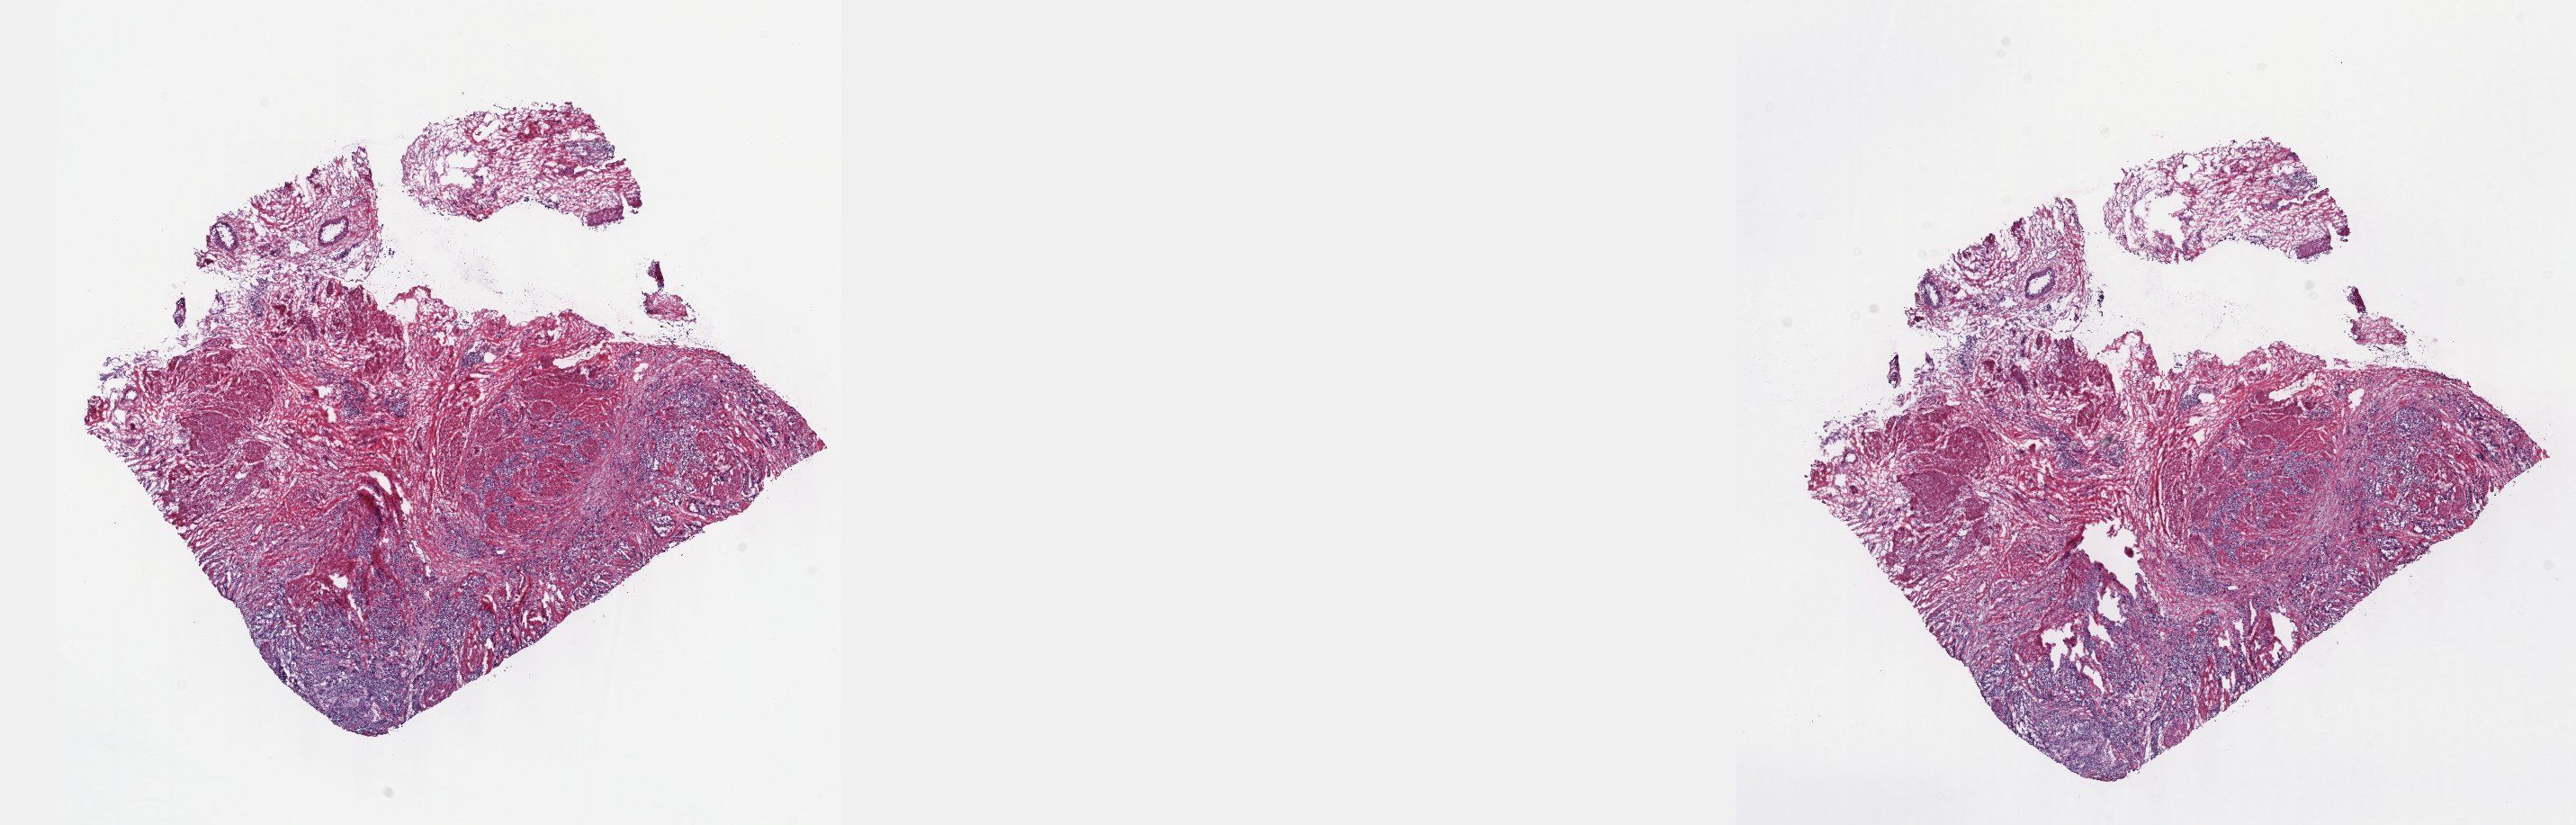
Whole-slide histology image, H&E, a low-resolution overview of the entire scanned area, about 23.1 x 7.4 mm. Frozen section from the top of the tissue portion. Sample: primary tumour, bladder. Male patient; age at initial diagnosis 85 years. Histologic grade: high grade. Pathologist review of this section (percent, as recorded): tumour cells 70%, tumour nuclei 70%, normal cells 0%, stromal cells 30%, necrosis 0%. Inflammatory infiltration, as recorded: lymphocyte infiltration 3%, monocyte infiltration 2%, neutrophil infiltration 5%.
Lymph nodes positive (case pathology): 4 of 19 examined. AJCC pathologic stage: IV (6th edition). Diagnosis: Transitional cell carcinoma. TNM: T3b N2 MX.